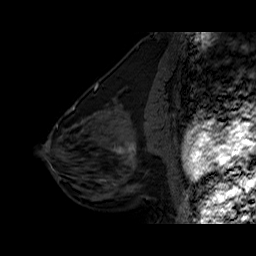
Breast MRI (dynamic contrast-enhanced), one sagittal slice. Slice 26 of 60 in the series (ordered by position). Dynamic contrast-enhanced series, time point 2 of 6 at this slice position (early post-contrast). 1.5 T. TE 6.3 ms, TR 32.5 ms. 256 × 256 image matrix, field of view 200 × 200 mm. Female patient. From the clinical record (not read from this slice): setting: breast cancer imaged before/during neoadjuvant chemotherapy; receptor status: triple-negative.
Annotated regions visible in this slice (semi-automatic segmentation, software-assisted and operator-edited):
- analysis volume of interest (the breast-tissue region the enhancement analysis was run in; not a lesion): bounding box [x1, y1, x2, y2] px = [102, 127, 162, 186]
- tumour enhancement mask (voxels above the 100 % enhancement threshold inside the analysis volume of interest): [114, 141, 136, 169]